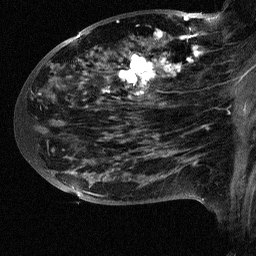
Breast MRI (dynamic contrast-enhanced), one sagittal slice. Position 34 of 64 along the scan axis. Dynamic contrast-enhanced study with each time point stored as its own series, time point 2 of 3 at this slice position (early post-contrast, ordered by acquisition time). 1.5 T. TE 4.5 ms, TR 11 ms. 2.5 mm slice thickness. 256 × 256 image matrix, field of view 200 × 200 mm. Female patient, age 38 years. From the clinical record (not read from this slice): setting: breast cancer imaged before/during neoadjuvant chemotherapy; receptor status: HR-positive, HER2-negative.
Annotated regions visible in this slice (semi-automatically segmented with operator editing):
- analysis volume of interest (the breast-tissue region the enhancement analysis was run in; not a lesion): bounding box <88,18,252,126> (left, top, right, bottom; pixels)
- tumour enhancement mask (voxels above the 90 % enhancement threshold inside the analysis volume of interest): <117,18,199,97>